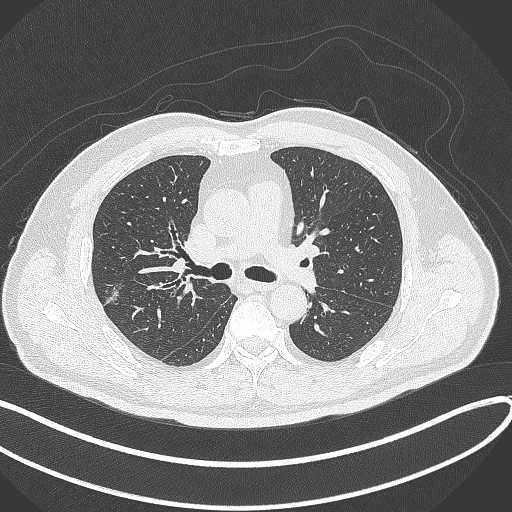
Chest CT, one axial slice. Slice 209 of 372 in the series (ordered by position). 120 kVp. Lung window (W 1500 / L -600 HU). 1 mm slice thickness. 512 × 512 image matrix, field of view 400 × 400 mm. Male patient, age 60 years. From the clinical record (not read from this slice): clinical TNM (as recorded): T1c N0 M0.
Structures marked on this image (bounding box drawn by a radiologist):
- lung tumour (recorded histology: adenocarcinoma): bounding box [x1, y1, x2, y2] px = [96, 278, 129, 309]